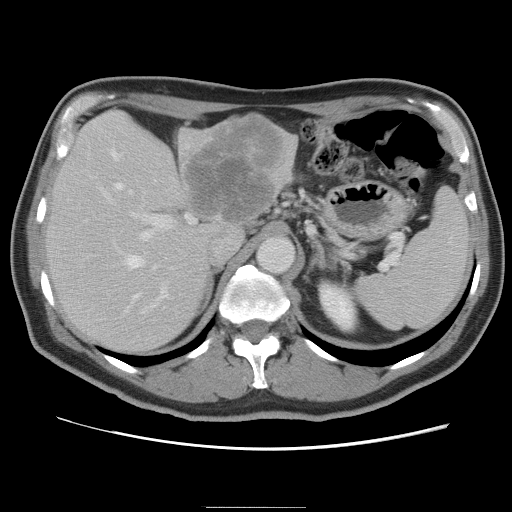
Contrast-enhanced abdominal CT, one axial slice. Slice 54 of 87 in the series (ordered by position). 120 kVp. Soft-tissue window (W 400 / L 40 HU). 5 mm slice thickness. 512 × 512 image matrix, field of view 363 × 363 mm. Male patient, age 63 years. From the clinical record (not read from this slice): diagnosis: colorectal cancer liver metastases, imaged before liver resection; multiple liver metastases: no; largest metastasis: 9 cm; disease in both lobes: no.
Annotated regions visible in this slice (outlined manually by an expert reader):
- hepatic veins: box from (x=111, y=151) to (x=157, y=312) px
- liver: (x=44, y=113)–(x=297, y=355)
- planned liver remnant (the part of the liver to remain after resection): (x=44, y=148)–(x=211, y=355)
- portal vein (with intrahepatic branches): (x=96, y=183)–(x=196, y=314)
- liver metastasis: (x=185, y=119)–(x=282, y=226)